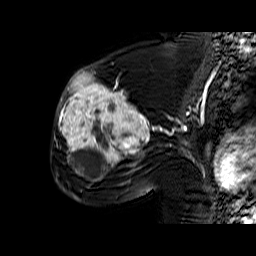
Breast MRI (dynamic contrast-enhanced), one sagittal slice; slice 35 of 60 in the series (ordered by position); dynamic contrast-enhanced series, time point 2 of 6 at this slice position (early post-contrast); 1.5 T; TE 6.4 ms, TR 32.9 ms; 4 mm slice thickness; 256 × 256 image matrix, field of view 200 × 200 mm. Female patient. Case-level facts recorded for this patient, not image findings: setting: breast cancer imaged before/during neoadjuvant chemotherapy; receptor status: triple-negative.
Annotated regions visible in this slice (semi-automatically segmented with operator editing):
- analysis volume of interest (the breast-tissue region the enhancement analysis was run in; not a lesion): bounding box [x1, y1, x2, y2] px = [57, 65, 159, 174]
- tumour enhancement mask (voxels above the 100 % enhancement threshold inside the analysis volume of interest): [57, 71, 153, 174]